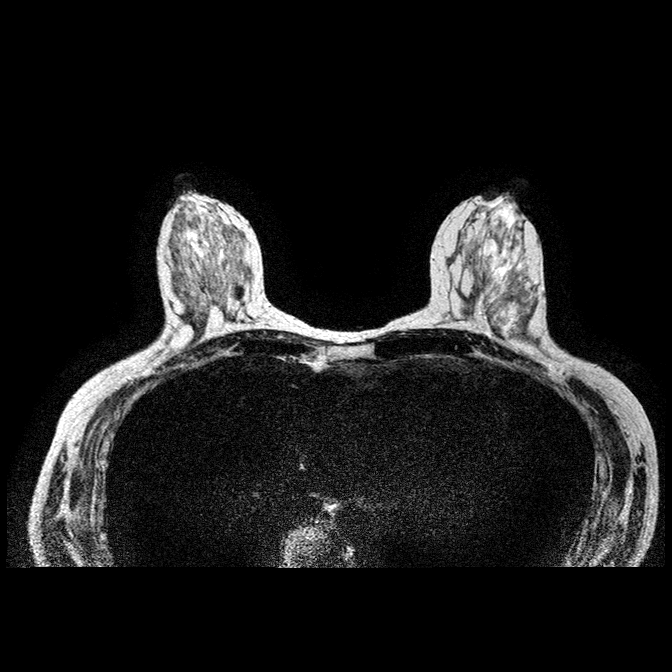
Breast MRI examination; 1 image, one mid-volume slice chosen by position. Age decade 60s.
Image 1: fluid-sensitive (T2/STIR) axial slice, series "T2W_TSE AX", slice 43 of 84.
MRI impression (as recorded): non-contrast exam. LEFT BREAST: The known left upper outer breast mass measures on the
noncontrast enhanced images approximately 5.2 x 3.1 x 2.5 cm. There isa thin fat line between posterior aspect of the mass and pectoral muscle. The distance between mass and pectoral muscle is less than 2 mm. In the left axilla there is the known malignant lymph node seen measuring 2.1 x 1.7 cm.
RIGHT BREAST: In the right upper inner breast there is a T2
hypointense rounded nodule seen measuring 5 x 6 mm. This is possible the correlate to the mammographic nodule with microcalcifications which could not to be stereotactically biopsied due to the superficial location. On MR the distance from this nodule to the skin is 8 mm. A second nodule, strongly T2 hypointense in the right central medial posterior breast is most likely the correlate of the mammographic nodule with coarse benign appearing calcifications.. There is no skin
thickening, nipple inversion, or right axillary lymphadenopathy
present.
1) Known 5.2 x 3.1 x 2.5 cm left upper outer breast mass with proximity to the pectoral muscle and malignant left axillary 2 cm lymph node. 2) 5 x 6 mm right upper inner breast nodule likely the correlate of themammographic nodule with associated microcalcifications,; BI-RADS 6.
Patient-level pathology facts (from the clinical record, not from the images): pathology diagnosis: invasive ductal (left breast); receptor status (as recorded): ER weak, PR weak, HER2 neg; Ki-67 (as recorded): high prolif; pathology report notes: Left breast: INVASIVE DUCTAL CARCINOMA, MODIFIED SCARFF-BLOOM-RICHARDSON GRADE-III/III.